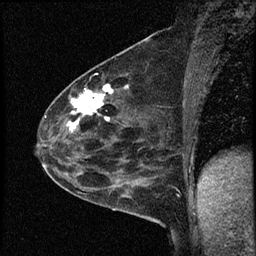
Breast MRI (dynamic contrast-enhanced), one sagittal slice; slice 37 of 60 in the series (ordered by position); dynamic contrast-enhanced study with each time point stored as its own series, time point 2 of 4 at this slice position (early post-contrast, ordered by acquisition time); 1.5 T; TE 4.2 ms, TR 17.6 ms; 2 mm slice thickness; 256 × 256 image matrix. Patient: female, 53 years. From the clinical record (not read from this slice): setting: breast cancer imaged before/during neoadjuvant chemotherapy; receptor status: HR-positive, HER2-negative.
Annotated regions visible in this slice (semi-automatic segmentation, software-assisted and operator-edited):
- analysis volume of interest (the breast-tissue region the enhancement analysis was run in; not a lesion): bounding box <42,69,156,199> (left, top, right, bottom; pixels)
- tumour enhancement mask (voxels above the 100 % enhancement threshold inside the analysis volume of interest): <67,85,128,131>